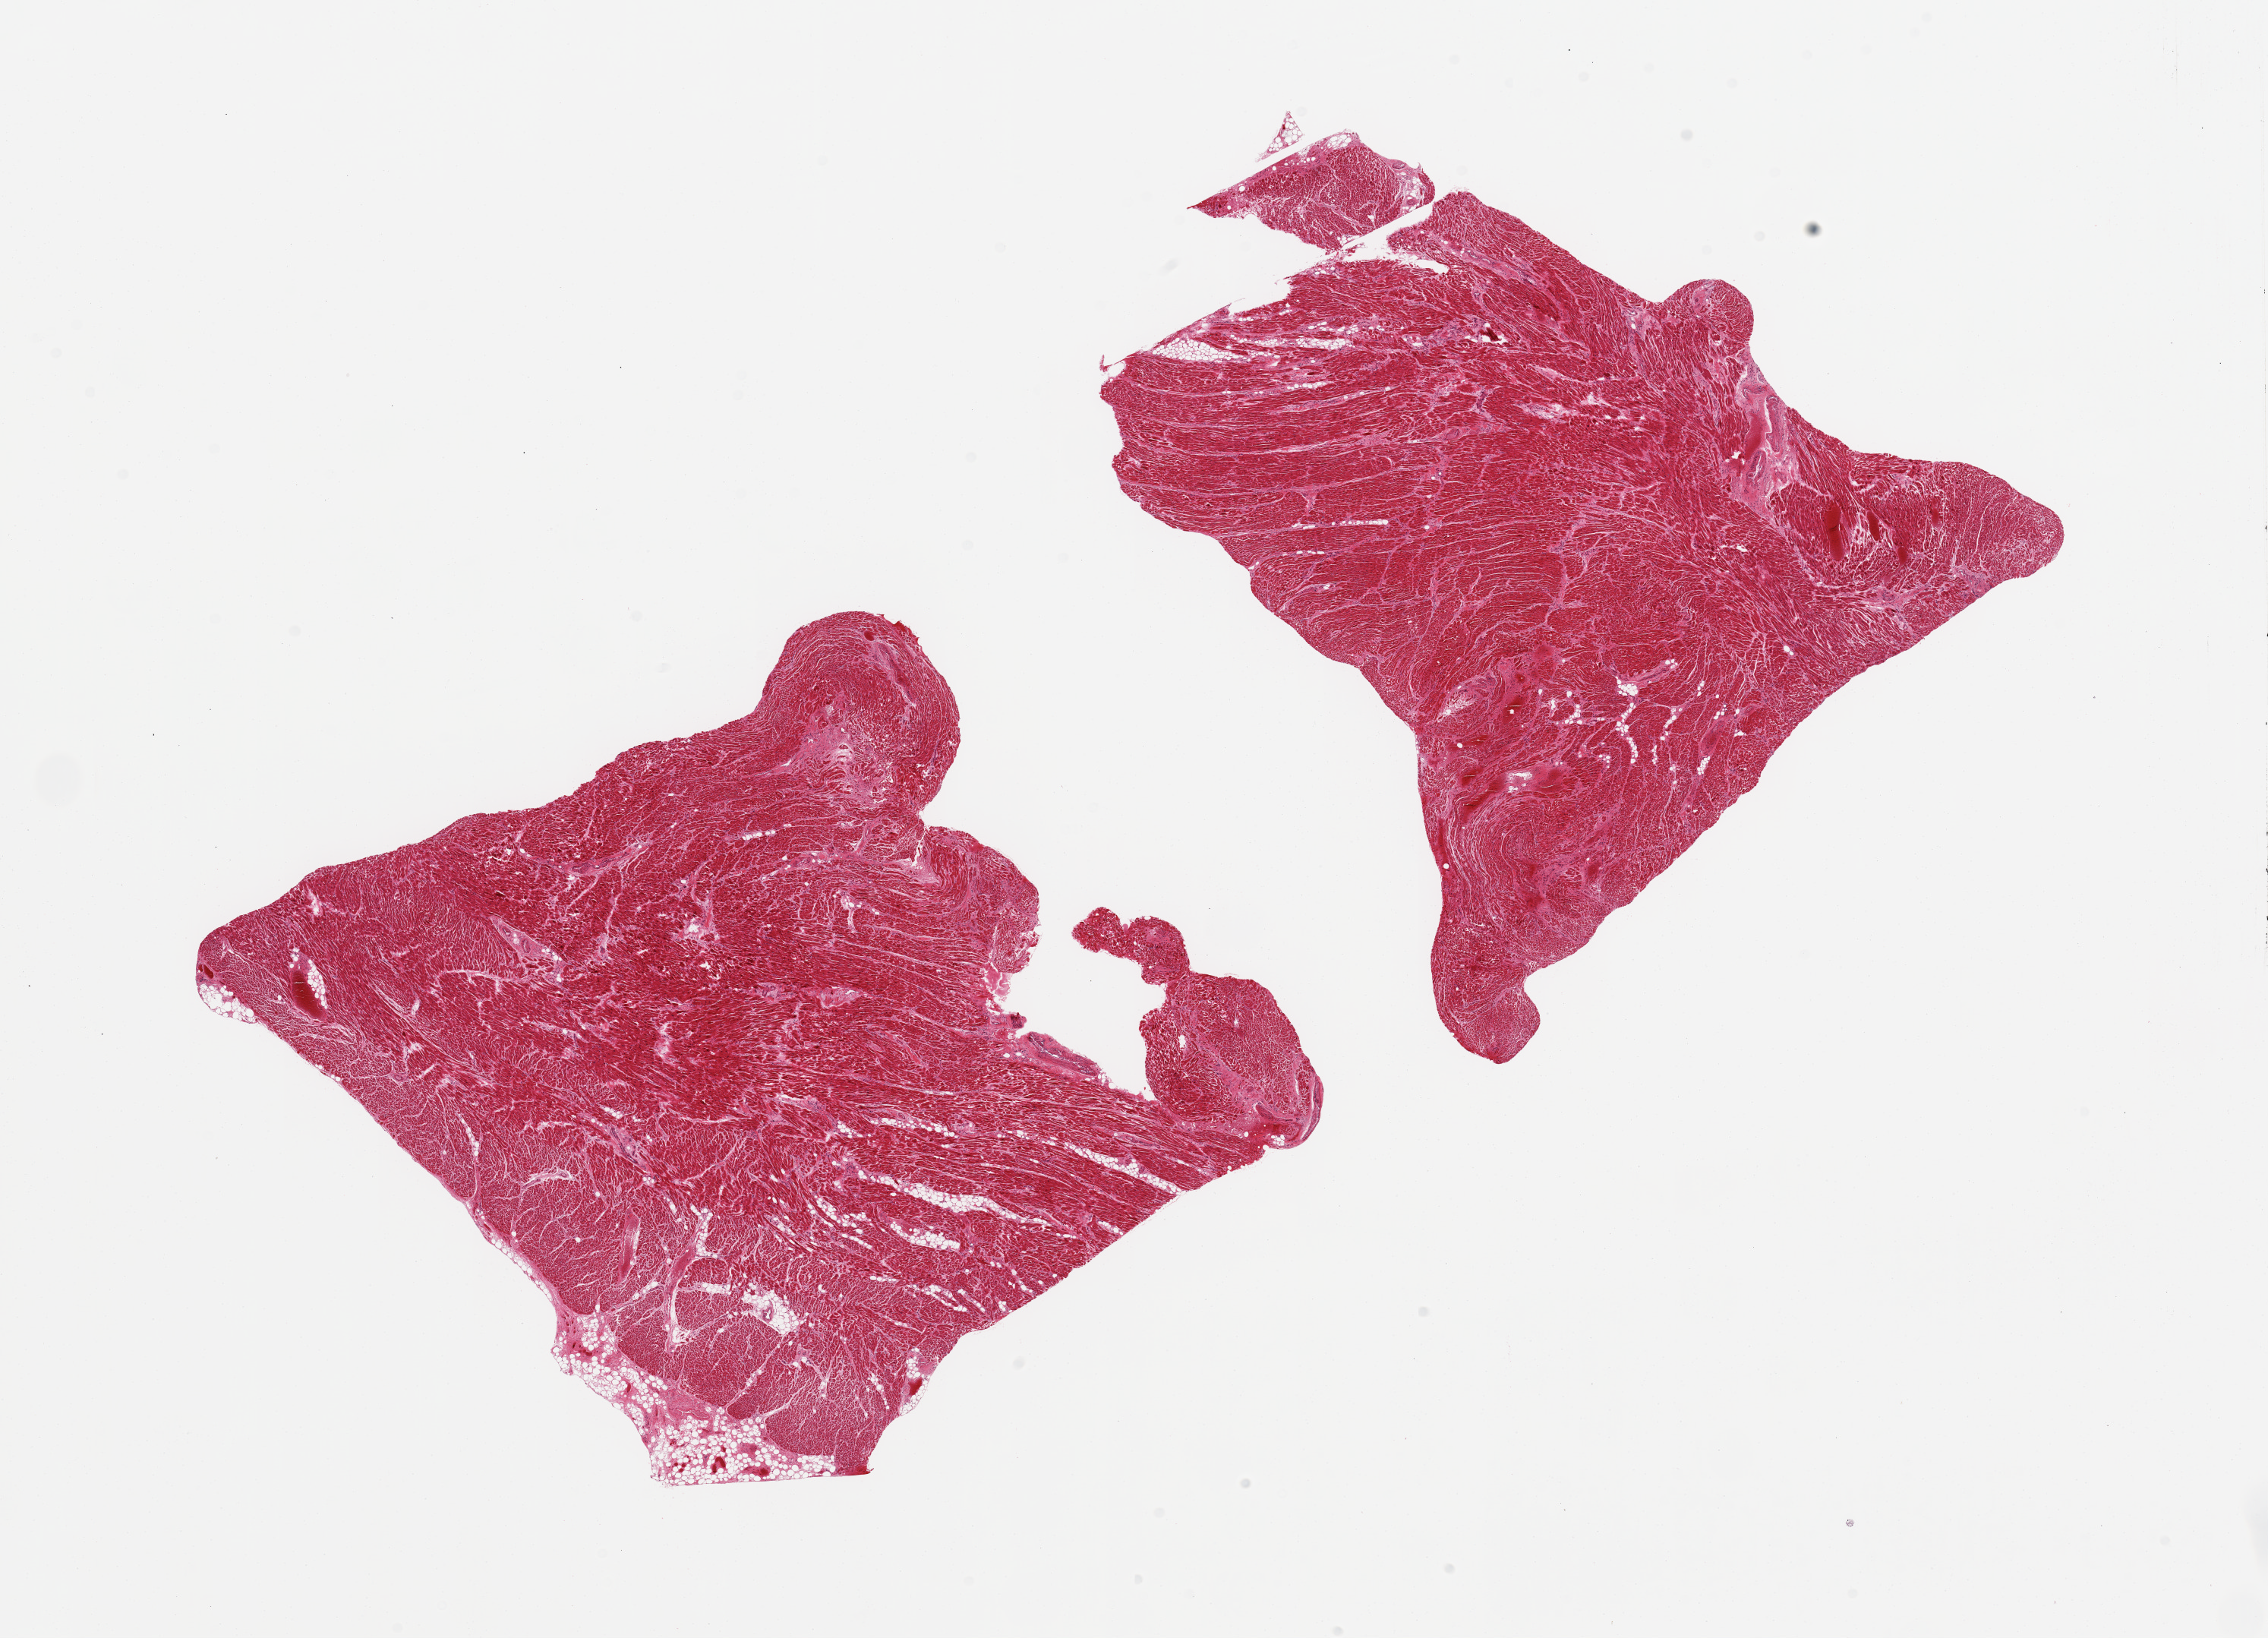
H&E whole-slide image — low-resolution overview of the scanned area, about 23.6 x 17.1 mm (acquisition: 20x scan); PAXgene-fixed paraffin-embedded (PFPE) section; section of heart (target tissue); donor tissue sample. Donor sex: female.
Review note (as recorded): 2 pieces; patchy hypereosinophilia (possible ischemia); focal hemorrhage.